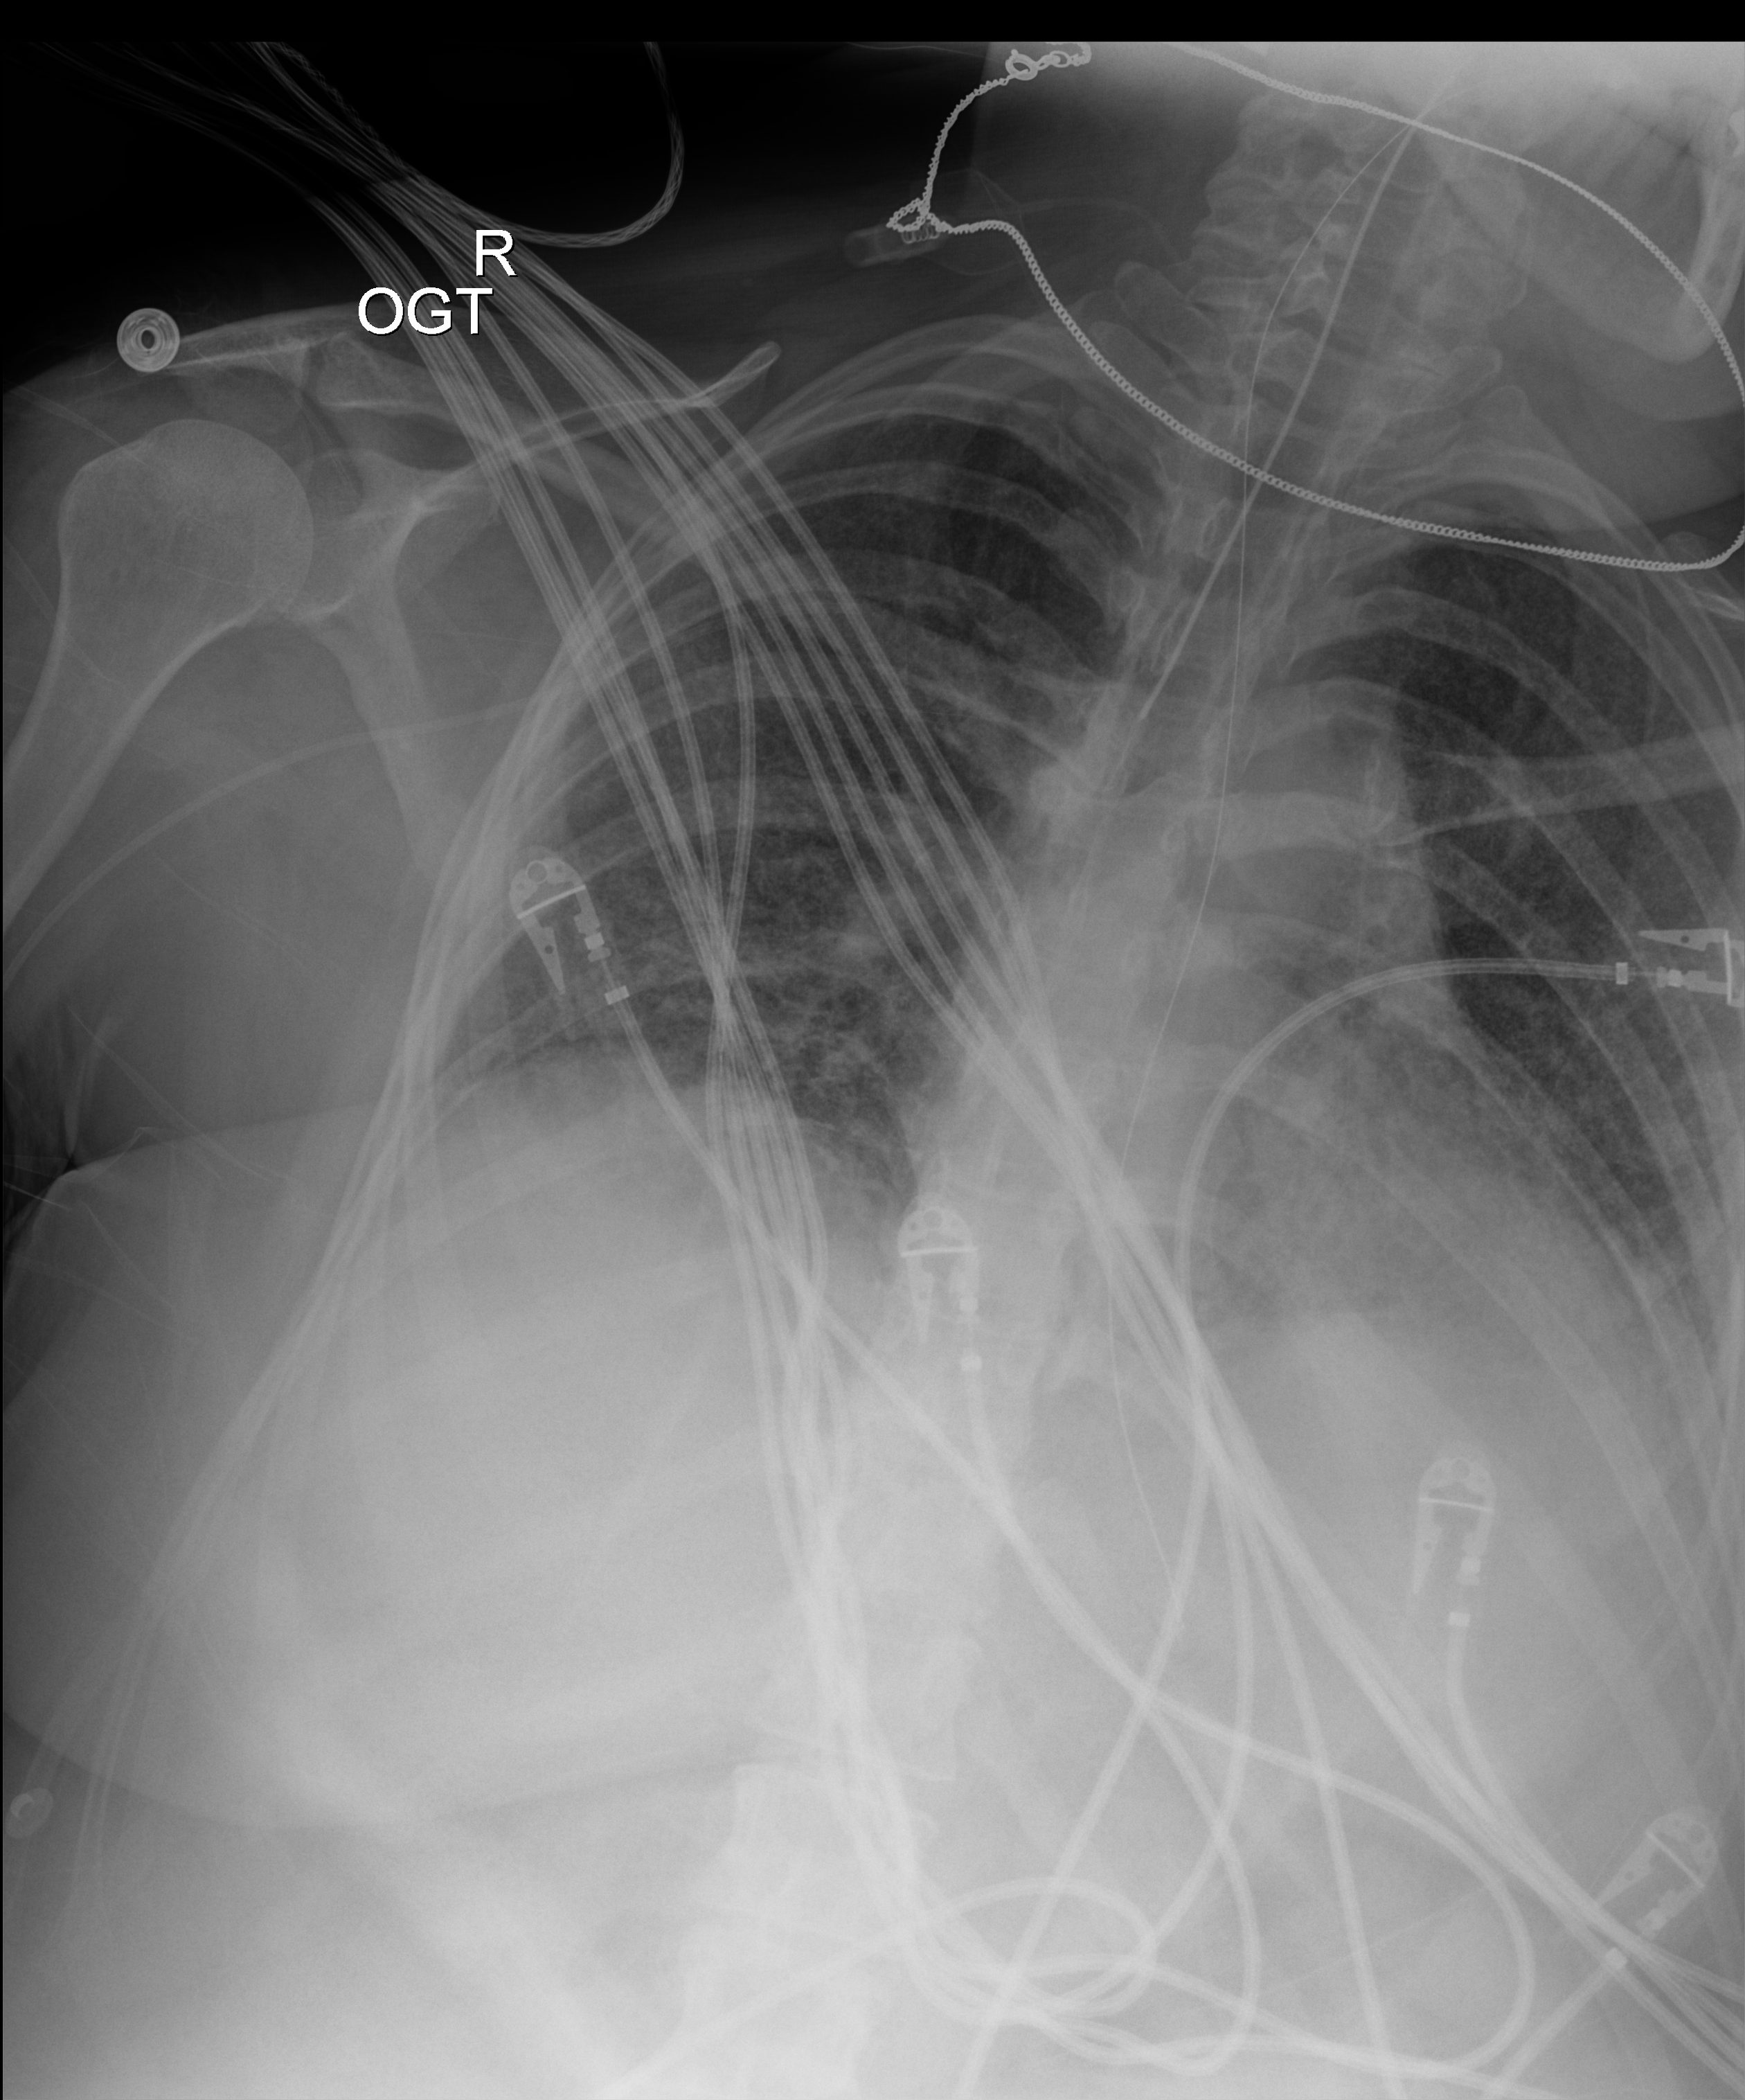
Chest X-ray (portable); anteroposterior (AP) projection. Patient hospitalised with COVID-19; female, aged 18–59 years.
Hospital-stay facts (about this admission, not read from this image; timing relative to this image not recorded):
- other chronic lung disease (admission record): yes
- mechanically ventilated during this hospital stay: yes
- length of hospital stay: 73 days